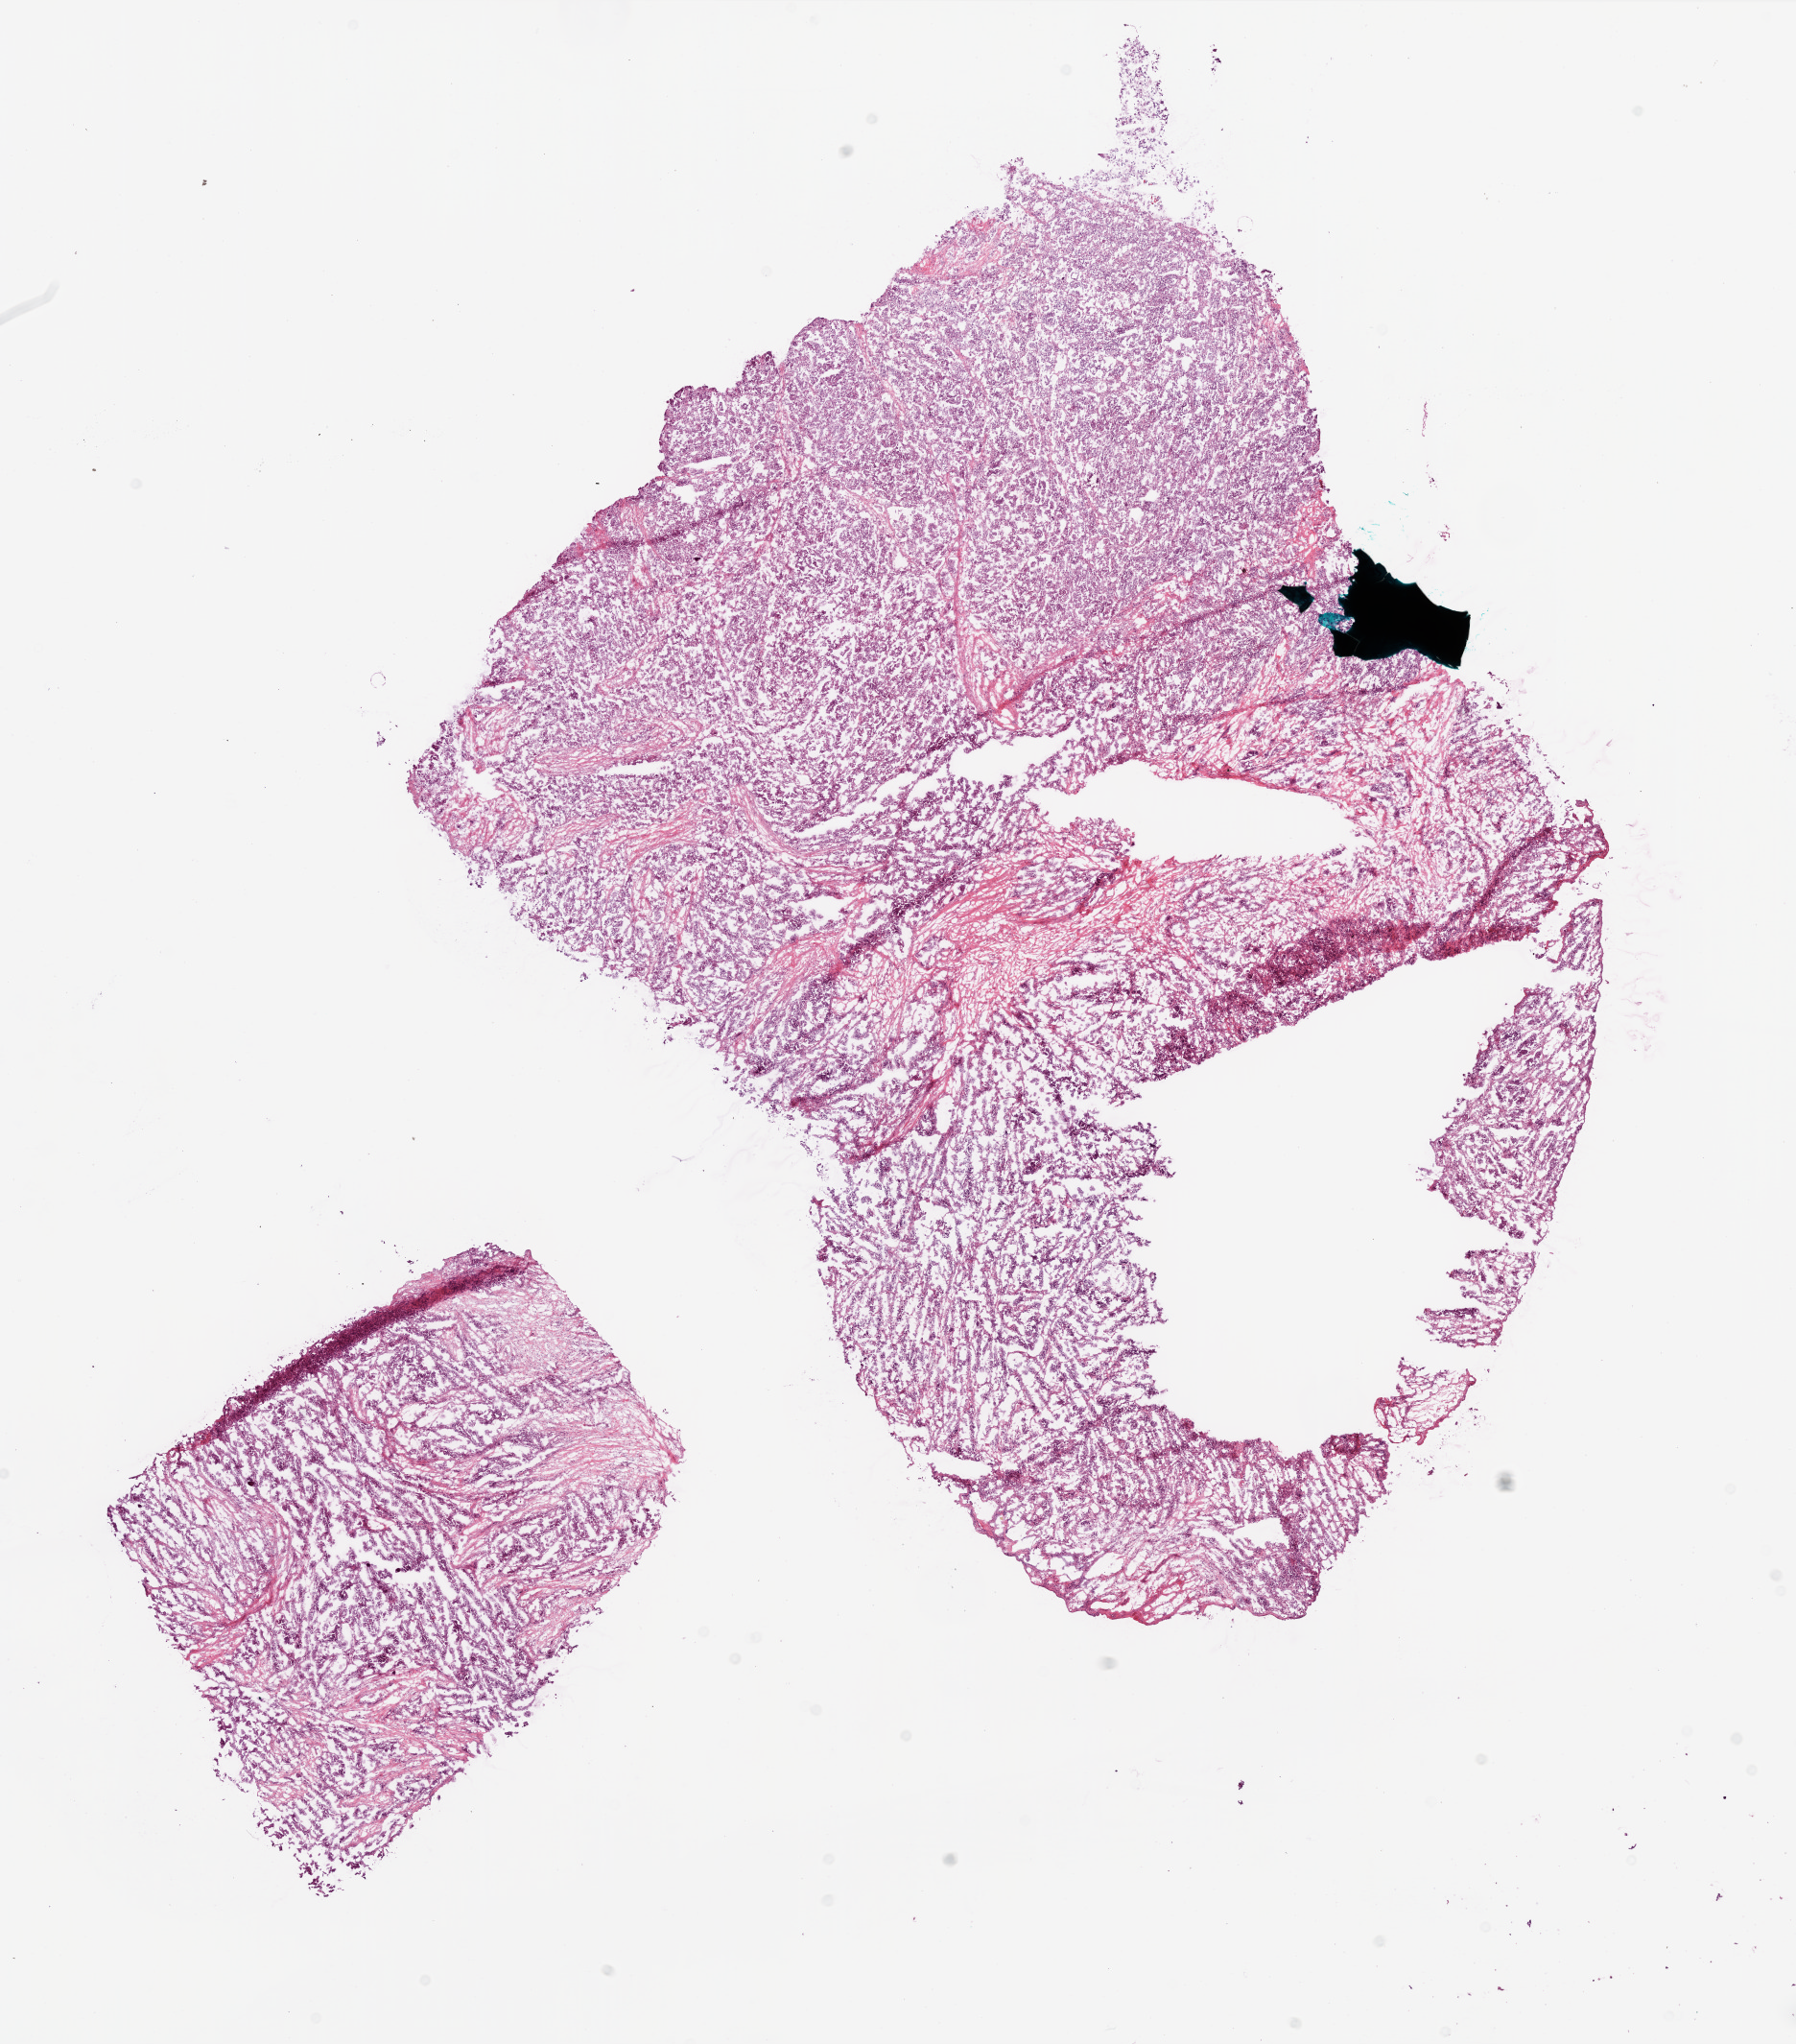
Digitized Hematoxylin and eosin (H&E) stained tissue section (whole slide), shown as a low-resolution overview of the whole scanned area (about 15.0 x 17.0 mm). Frozen section from the bottom of the tissue portion. Primary tumour sample from the ovary. Female, age 52 years at initial diagnosis. Histologic grade: G3 (poorly differentiated). Slide review estimates, as recorded: tumour cells 60%, tumour nuclei 70%, normal cells 0%, stromal cells 40%, necrosis 0%.
Pathologic diagnosis: Serous cystadenocarcinoma, NOS. FIGO stage: IIIC.